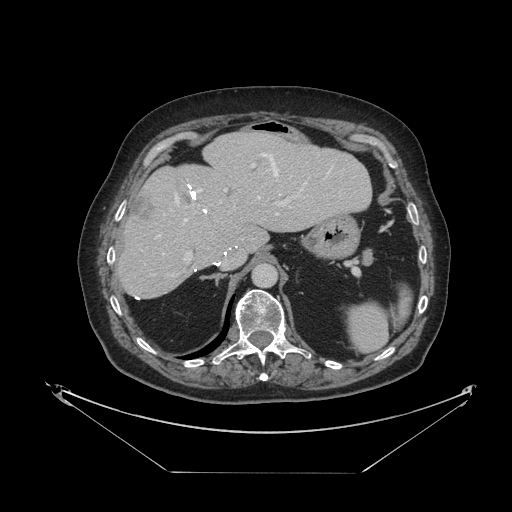
Contrast-enhanced abdominal CT, one axial slice. Position 72 of 121 along the scan axis. Intravenous contrast given. Soft-tissue window (W 400 / L 40 HU). 2.5 mm slice thickness. 512 × 512 image matrix, field of view 500 × 500 mm. Male patient, age 68 years. Case-level facts recorded for this patient, not image findings: diagnosis: colorectal cancer liver metastases, imaged before liver resection; multiple liver metastases: no.
Outlined on this slice (manually delineated by an expert):
- hepatic veins: box from (x=156, y=154) to (x=281, y=238) px
- liver: (x=119, y=132)–(x=371, y=299)
- planned liver remnant (the part of the liver to remain after resection): (x=119, y=132)–(x=371, y=299)
- portal vein (with intrahepatic branches): (x=168, y=164)–(x=296, y=277)
- liver metastasis: (x=132, y=195)–(x=156, y=223)